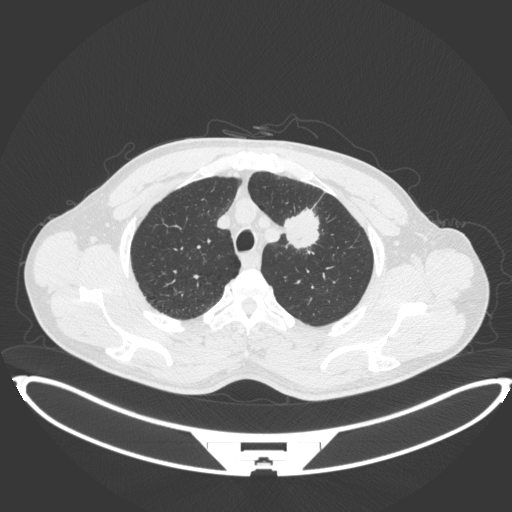
Chest CT, one axial slice; position 357 of 407 along the scan axis; reconstruction kernel B31f; lung window (W 1500 / L -600 HU); 512 × 512 image matrix. Male patient, age 60 years. From the clinical record (not read from this slice): clinical TNM (as recorded): T2a N0 M0.
Annotated regions visible in this slice (bounding box drawn by a radiologist):
- lung tumour (recorded histology: squamous cell carcinoma): bounding box (x1, y1, x2, y2) in pixels: (282, 203, 320, 250)